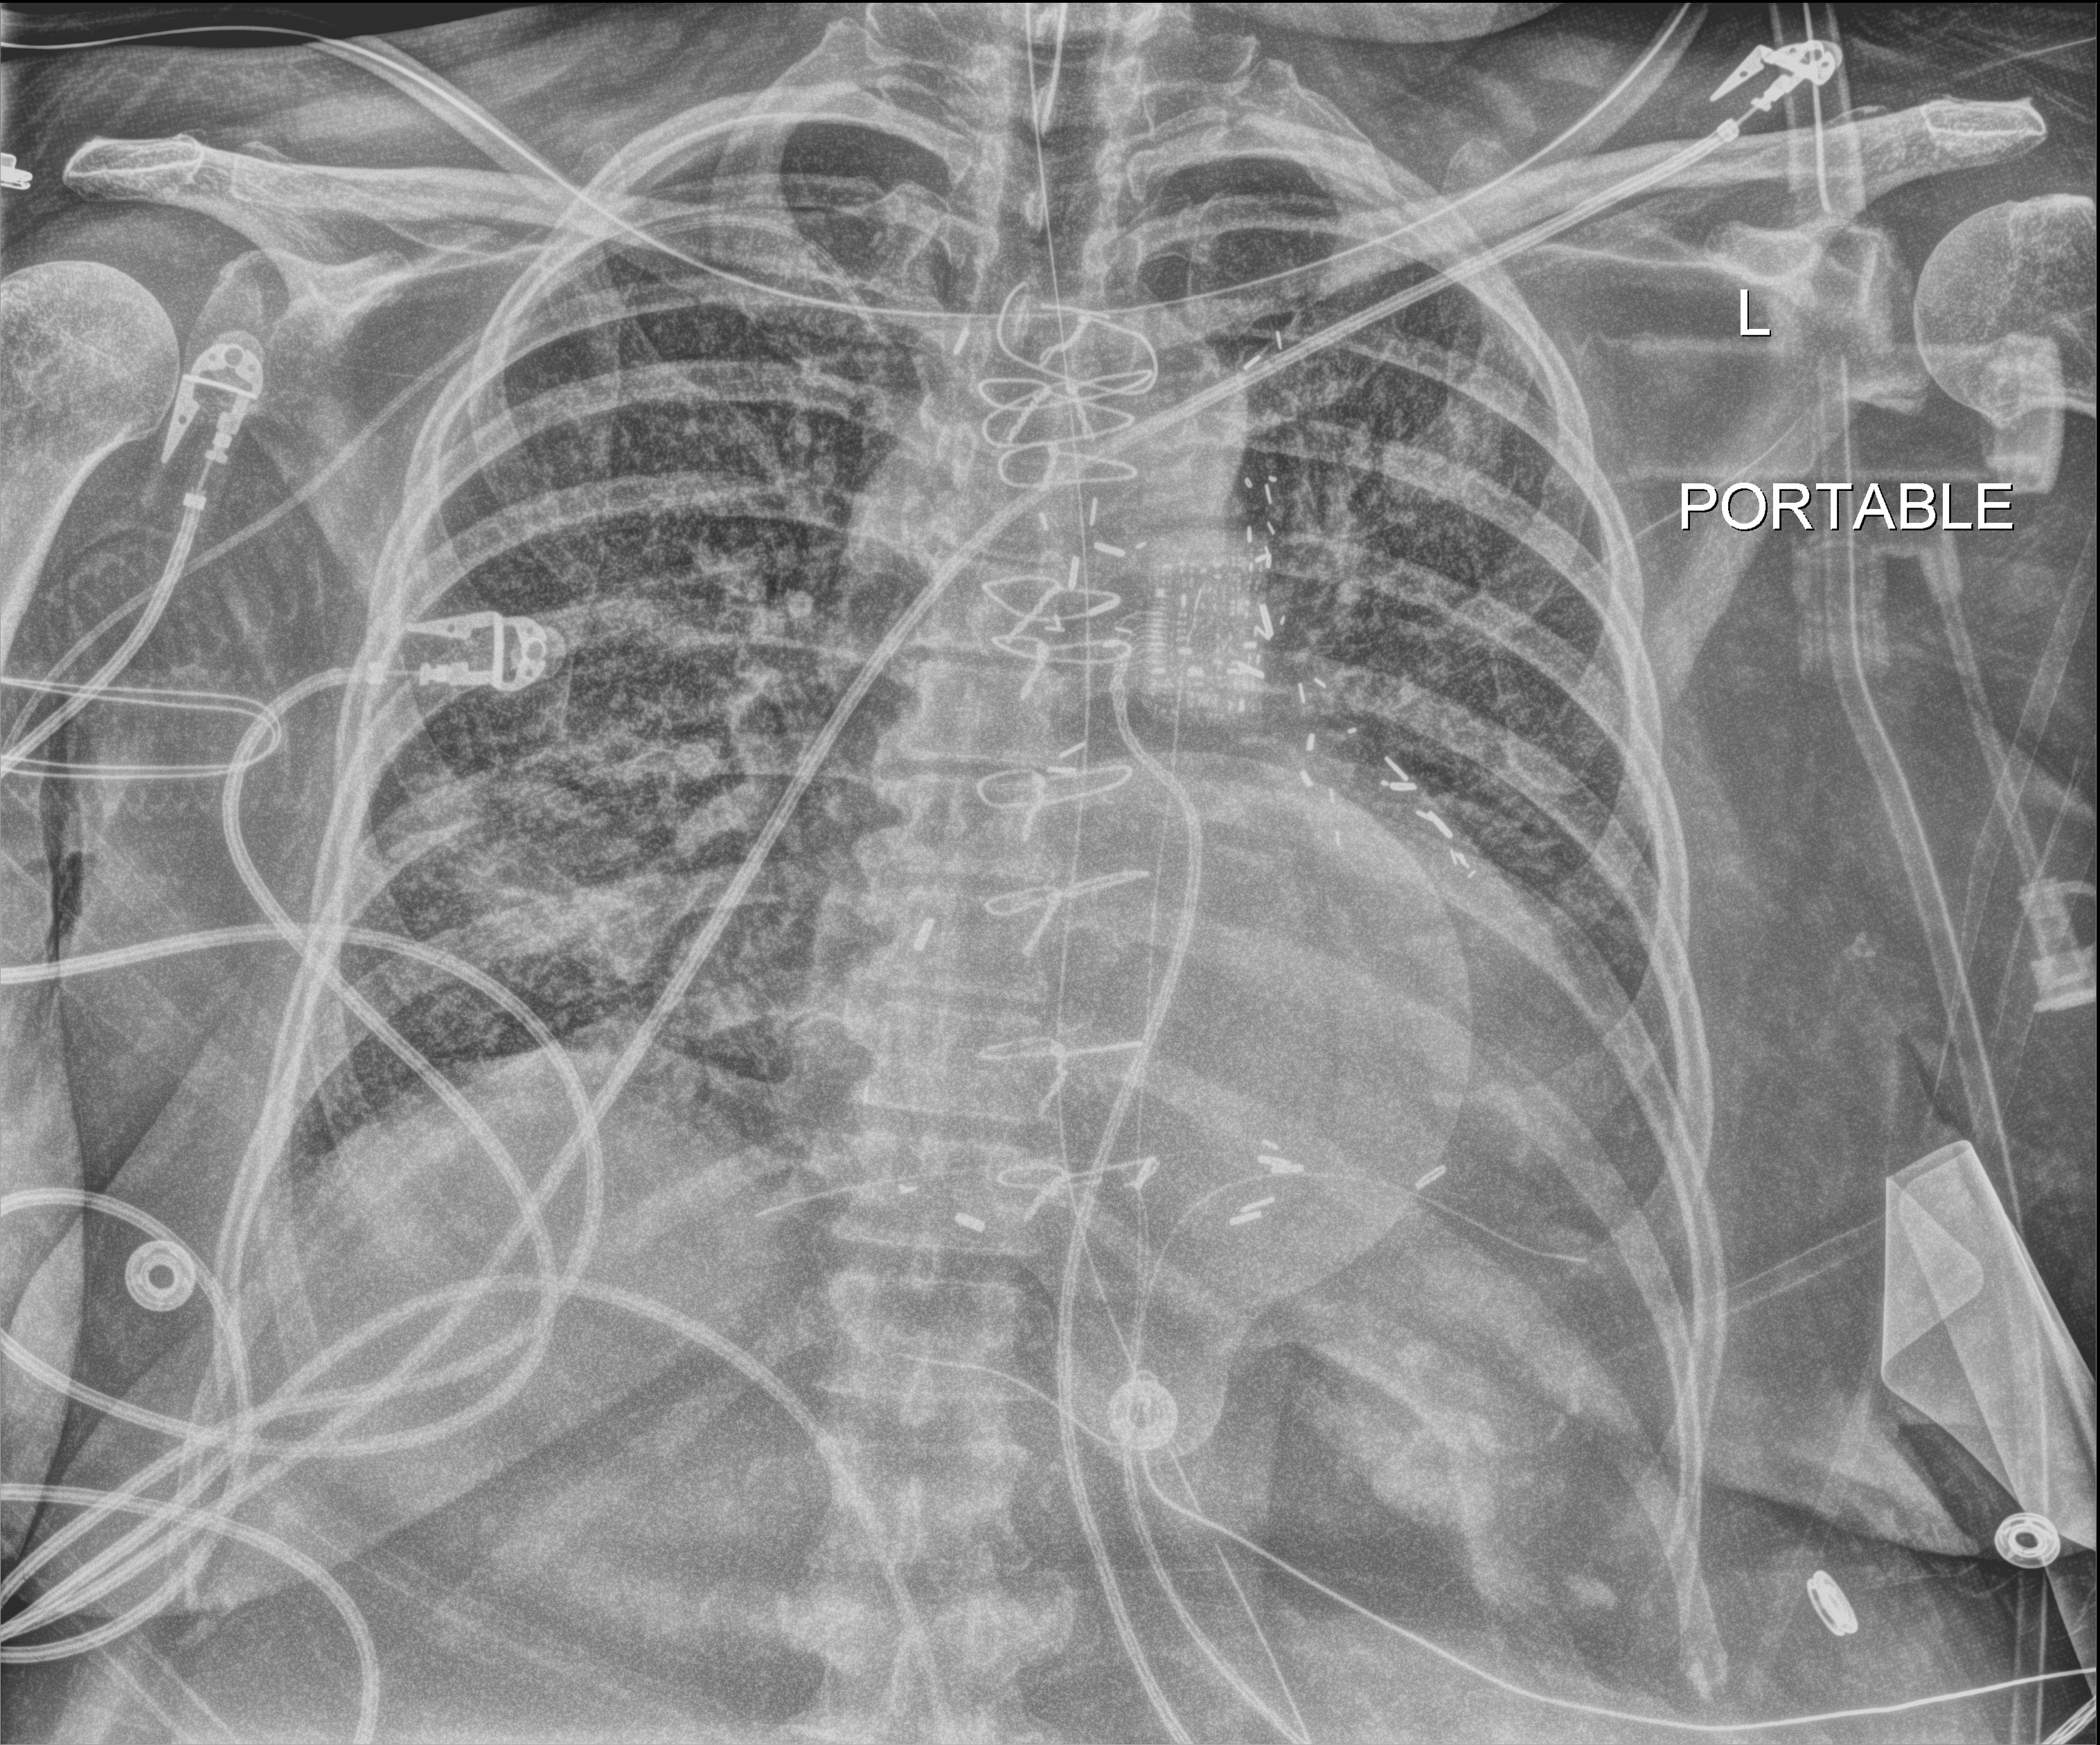
Portable chest radiograph; anteroposterior (AP) projection. Female patient hospitalised with COVID-19, age 60–74 years.
Hospital-stay facts (about this admission, not read from this image; timing relative to this image not recorded): chronic kidney disease (admission record): no; mechanically ventilated during this hospital stay: yes; hypertension (admission record): yes.